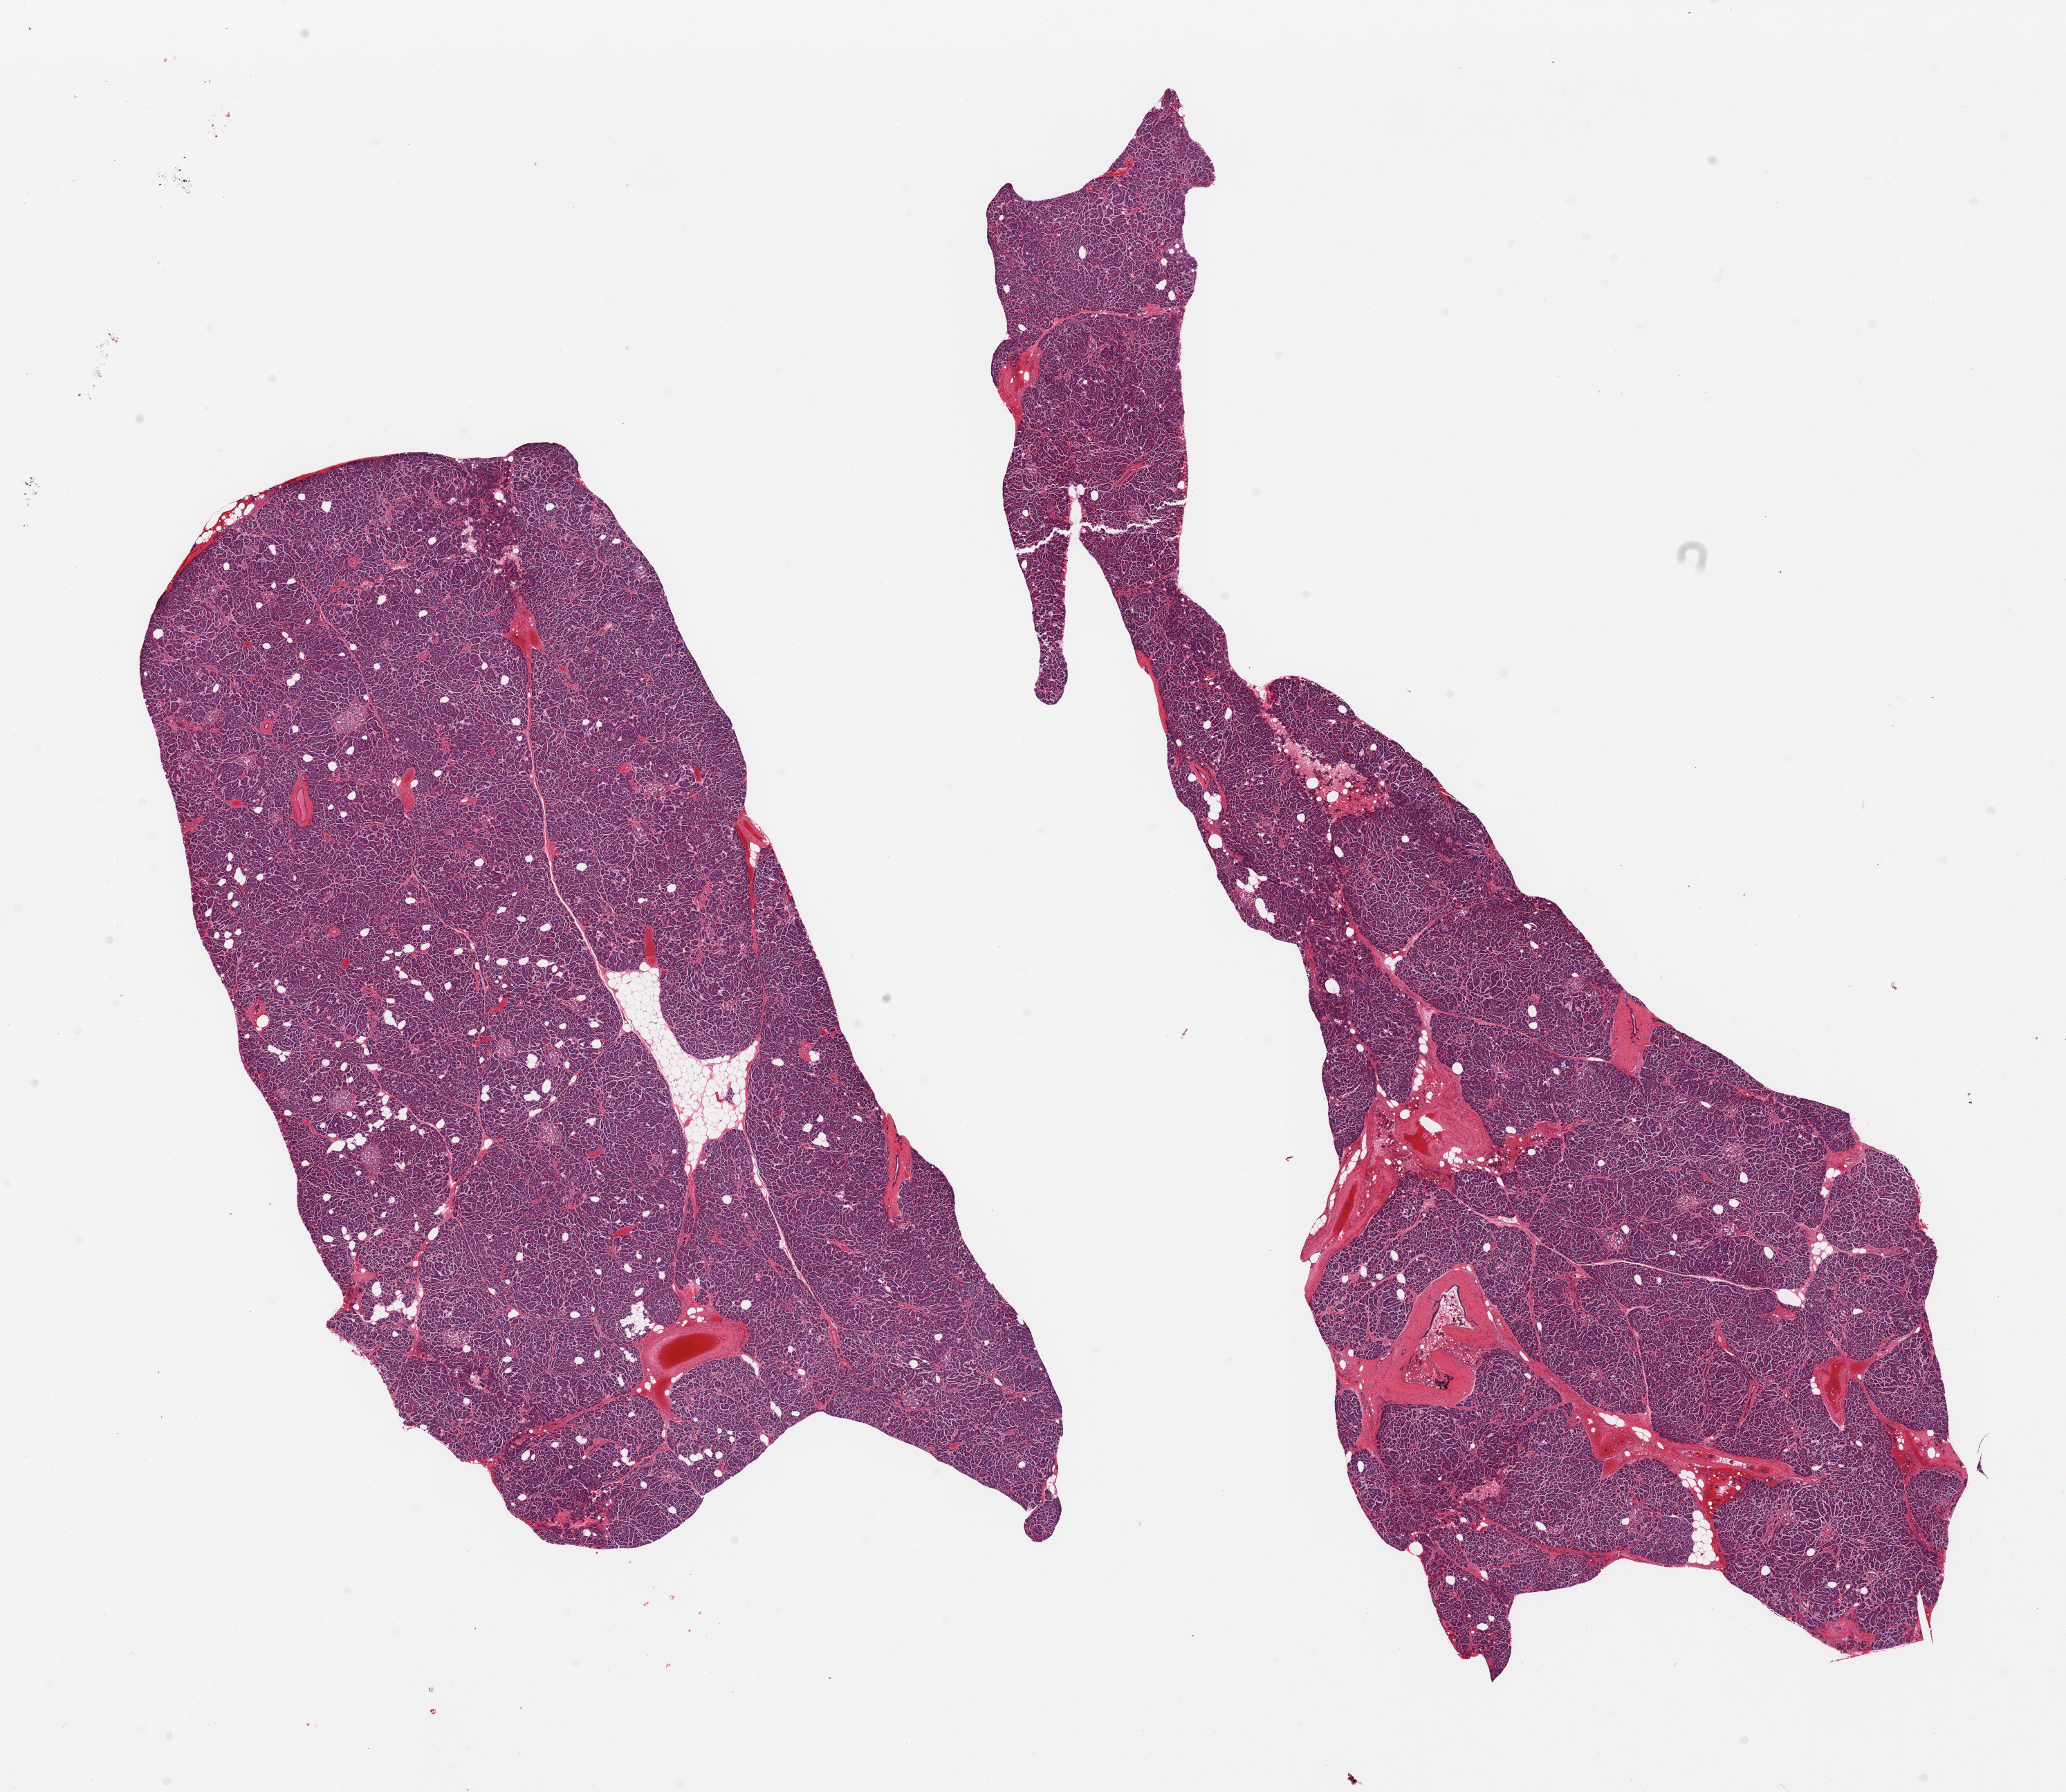
Whole-slide image, hematoxylin and eosin (H&E) stain — a low-resolution overview of the entire scanned area, about 23.6 x 20.5 mm. PAXgene-fixed paraffin-embedded (PFPE) section. Sampled site (target tissue): pancreas. Tissue donor sample. Donor sex: female.
* review note (as recorded): 2 pieces